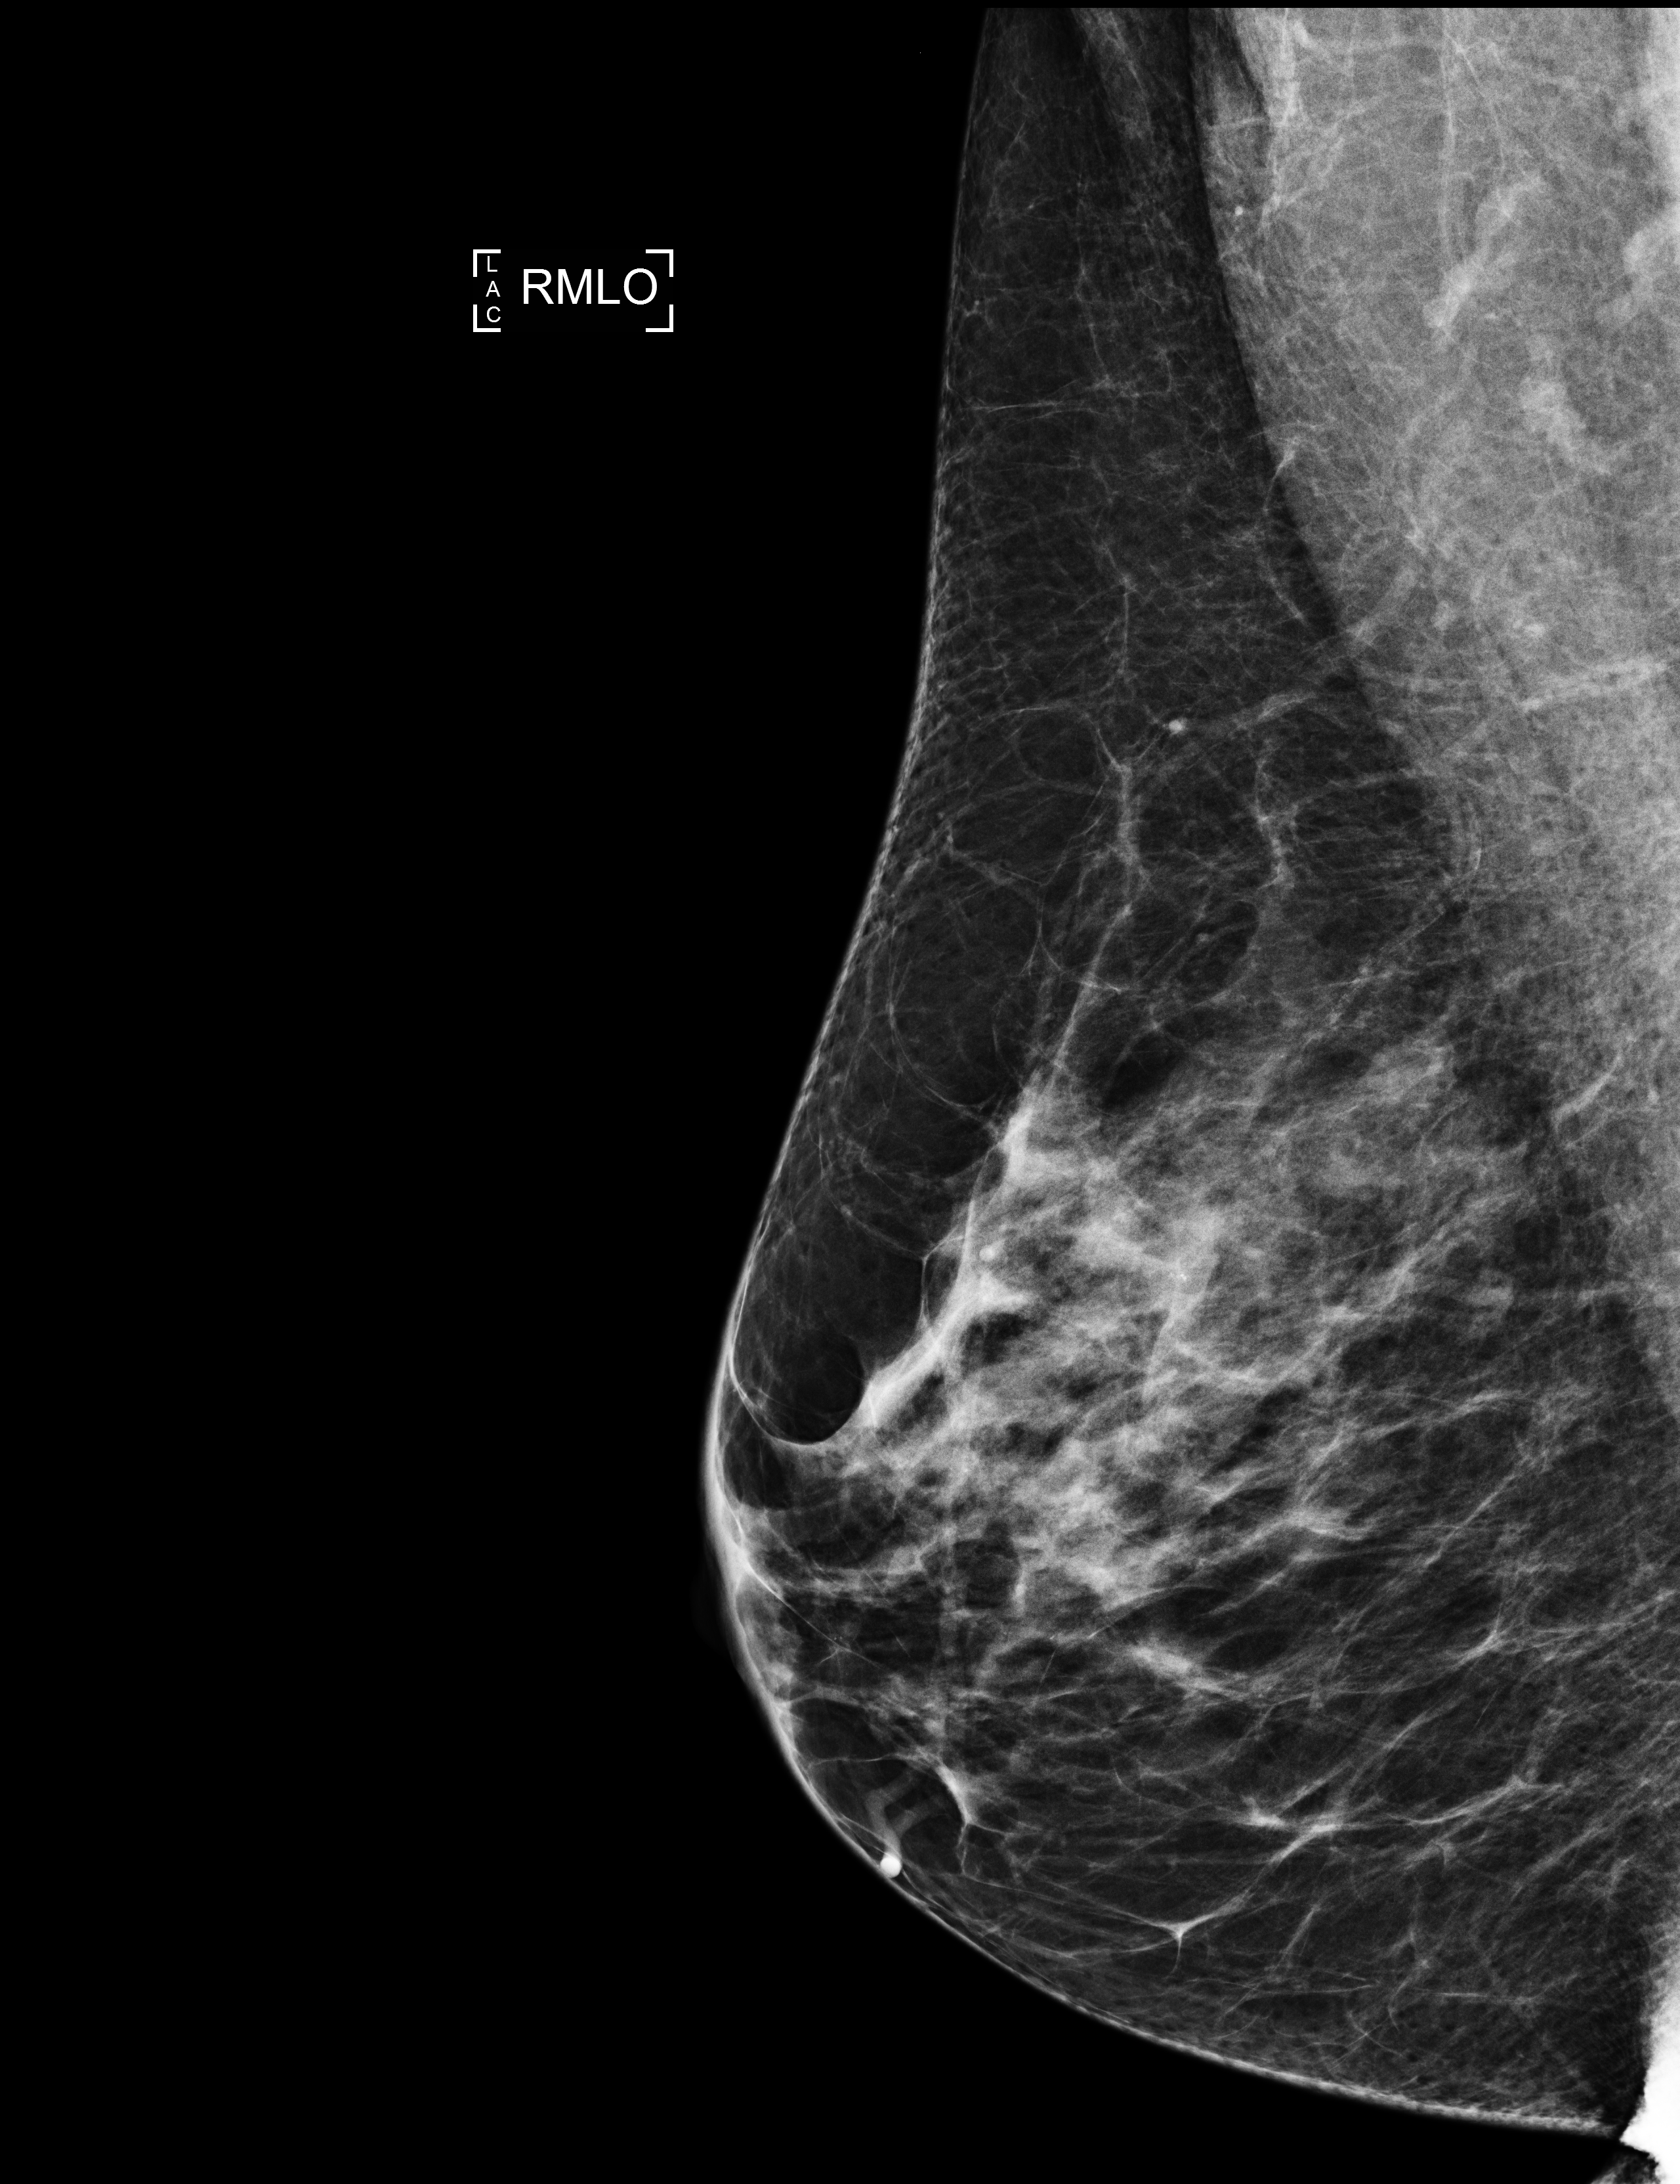
Annual screening mammography examination. Patient aged 63 years (female).
Image type: full-field digital mammogram. Breast: right. Projection: mediolateral oblique (MLO) view. BI-RADS breast density category at the screening exam (both breasts, scale 1–4): 3. Final BI-RADS assessment for this screening round (tomosynthesis exam, both breasts): category 1. Recall: recalled for additional imaging after this screen.